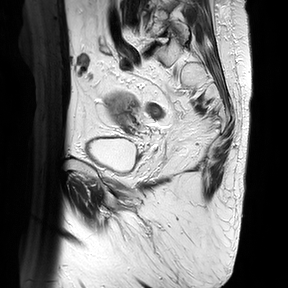
Pelvic MRI for cervical cancer, one sagittal slice; position 23 of 30 along the scan axis; T2-weighted; 1.5 T; TE 100 ms, TR 4816.3 ms; 288 × 288 image matrix. Female patient, age 74 years.
Outlined on this slice (outlined manually by an expert reader):
- uterus and cervix: box from (x=106, y=90) to (x=134, y=126) px